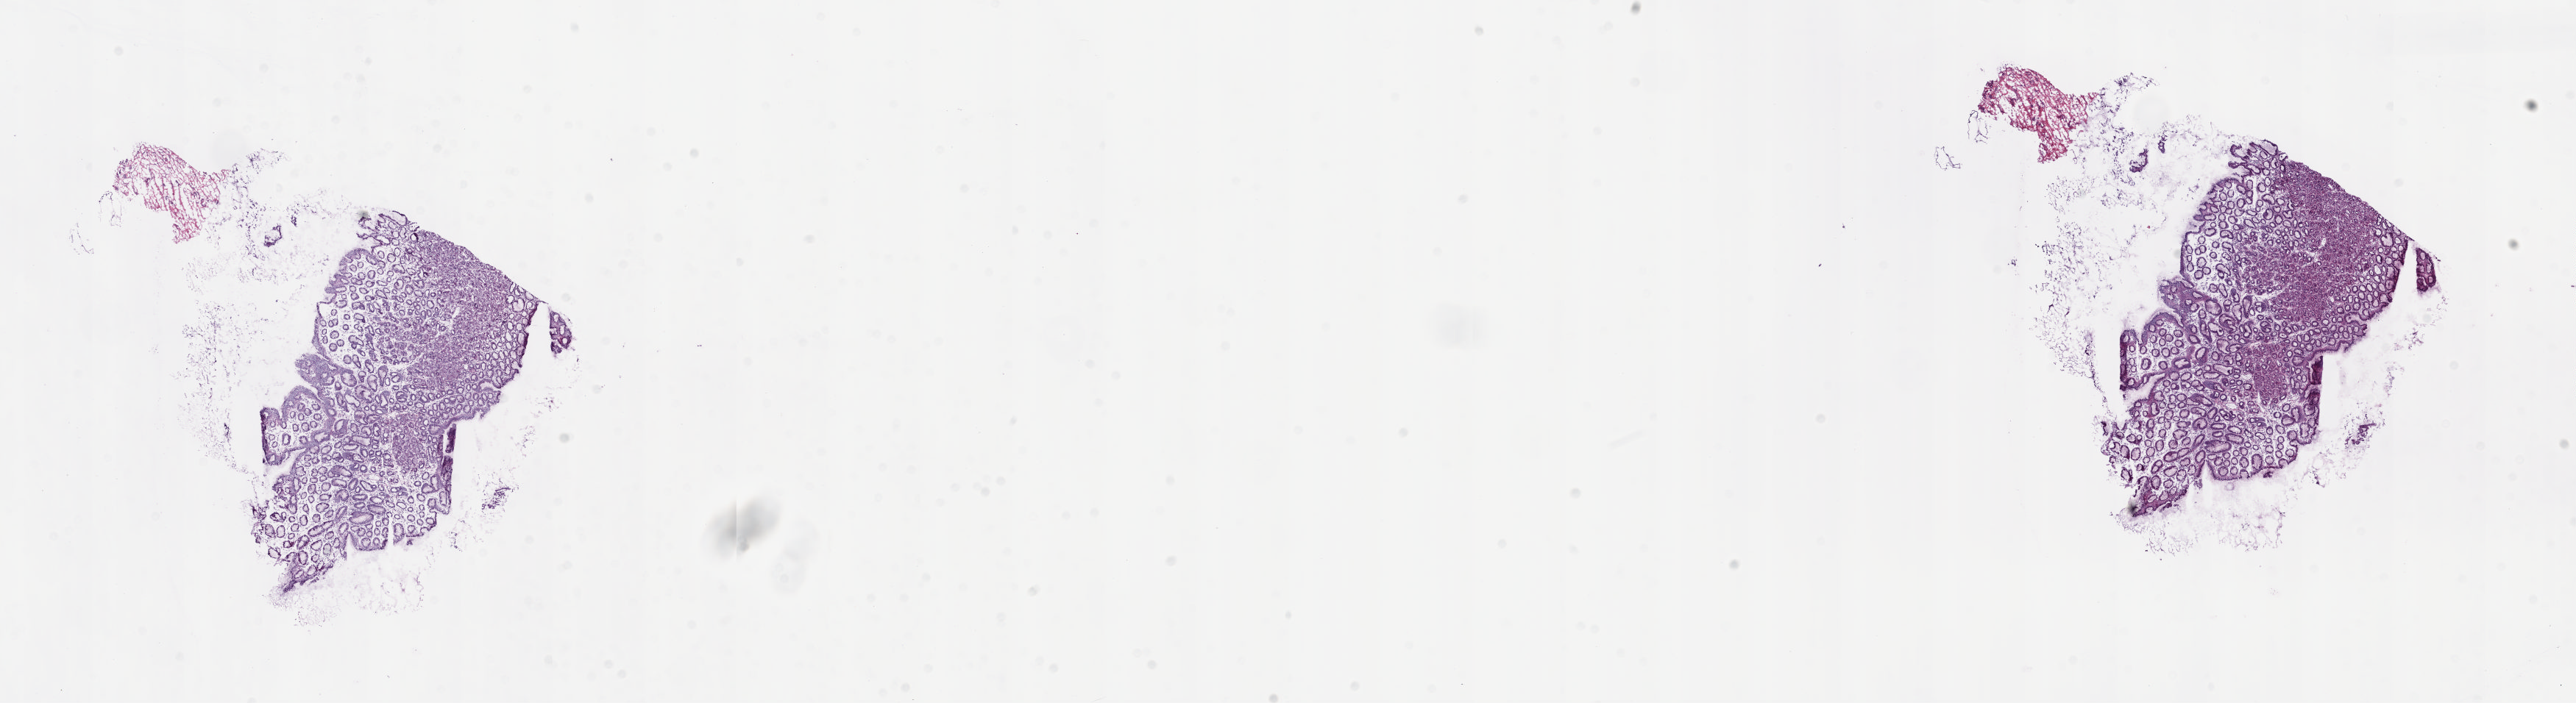
H&E-stained whole-slide image, whole scanned area (about 27.8 x 7.6 mm) shown as a low-resolution overview; frozen section from the top of the tissue portion; sample: solid tissue normal (non-tumour tissue), esophagus. Patient: male, age at initial diagnosis 71 years. Slide review estimates, as recorded: tumour cells 0%, tumour nuclei 0%, normal cells 100%, stromal cells 0%, necrosis 0%. Infiltration values recorded for this section: lymphocyte infiltration 0%, monocyte infiltration 0%, neutrophil infiltration 0%.
This section: solid tissue normal (non-tumour) sample from the same patient. Patient diagnosis: Squamous cell carcinoma, NOS (middle third of esophagus).